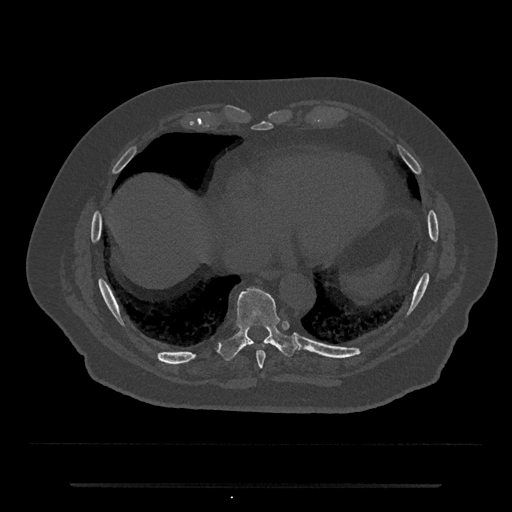
CT including the spine, one axial slice; position 771 of 797 along the scan axis; reconstruction kernel Br40s/3; 120 kVp; bone window (W 1800 / L 400 HU); 512 × 512 image matrix, field of view 434 × 434 mm. Male patient, age 80 years. From the clinical record (not read from this slice): primary cancer: prostate.
Structures marked on this image (semi-automatically segmented with operator editing):
- T8 vertebra: bounding box (x1, y1, x2, y2) in pixels: (256, 351, 265, 369)
- T9 vertebra: (217, 286, 301, 361)